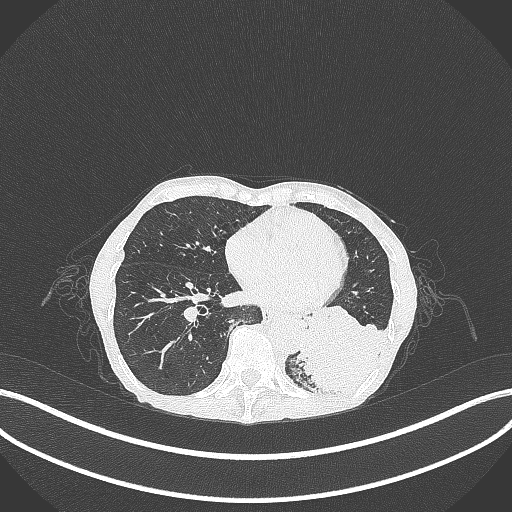
Chest CT, one axial slice. Position 93 of 347 along the scan axis. 120 kVp. Lung window (W 1500 / L -600 HU). 512 × 512 image matrix, field of view 400 × 400 mm. Patient: female, 70 years. Case-level facts recorded for this patient, not image findings: clinical TNM (as recorded): T3 N0 M0; histopathological grade: G3.
Structures marked on this image (rectangle marked by the reading radiologist):
- lung tumour (recorded histology: small cell carcinoma): box from (x=299, y=307) to (x=395, y=396) px